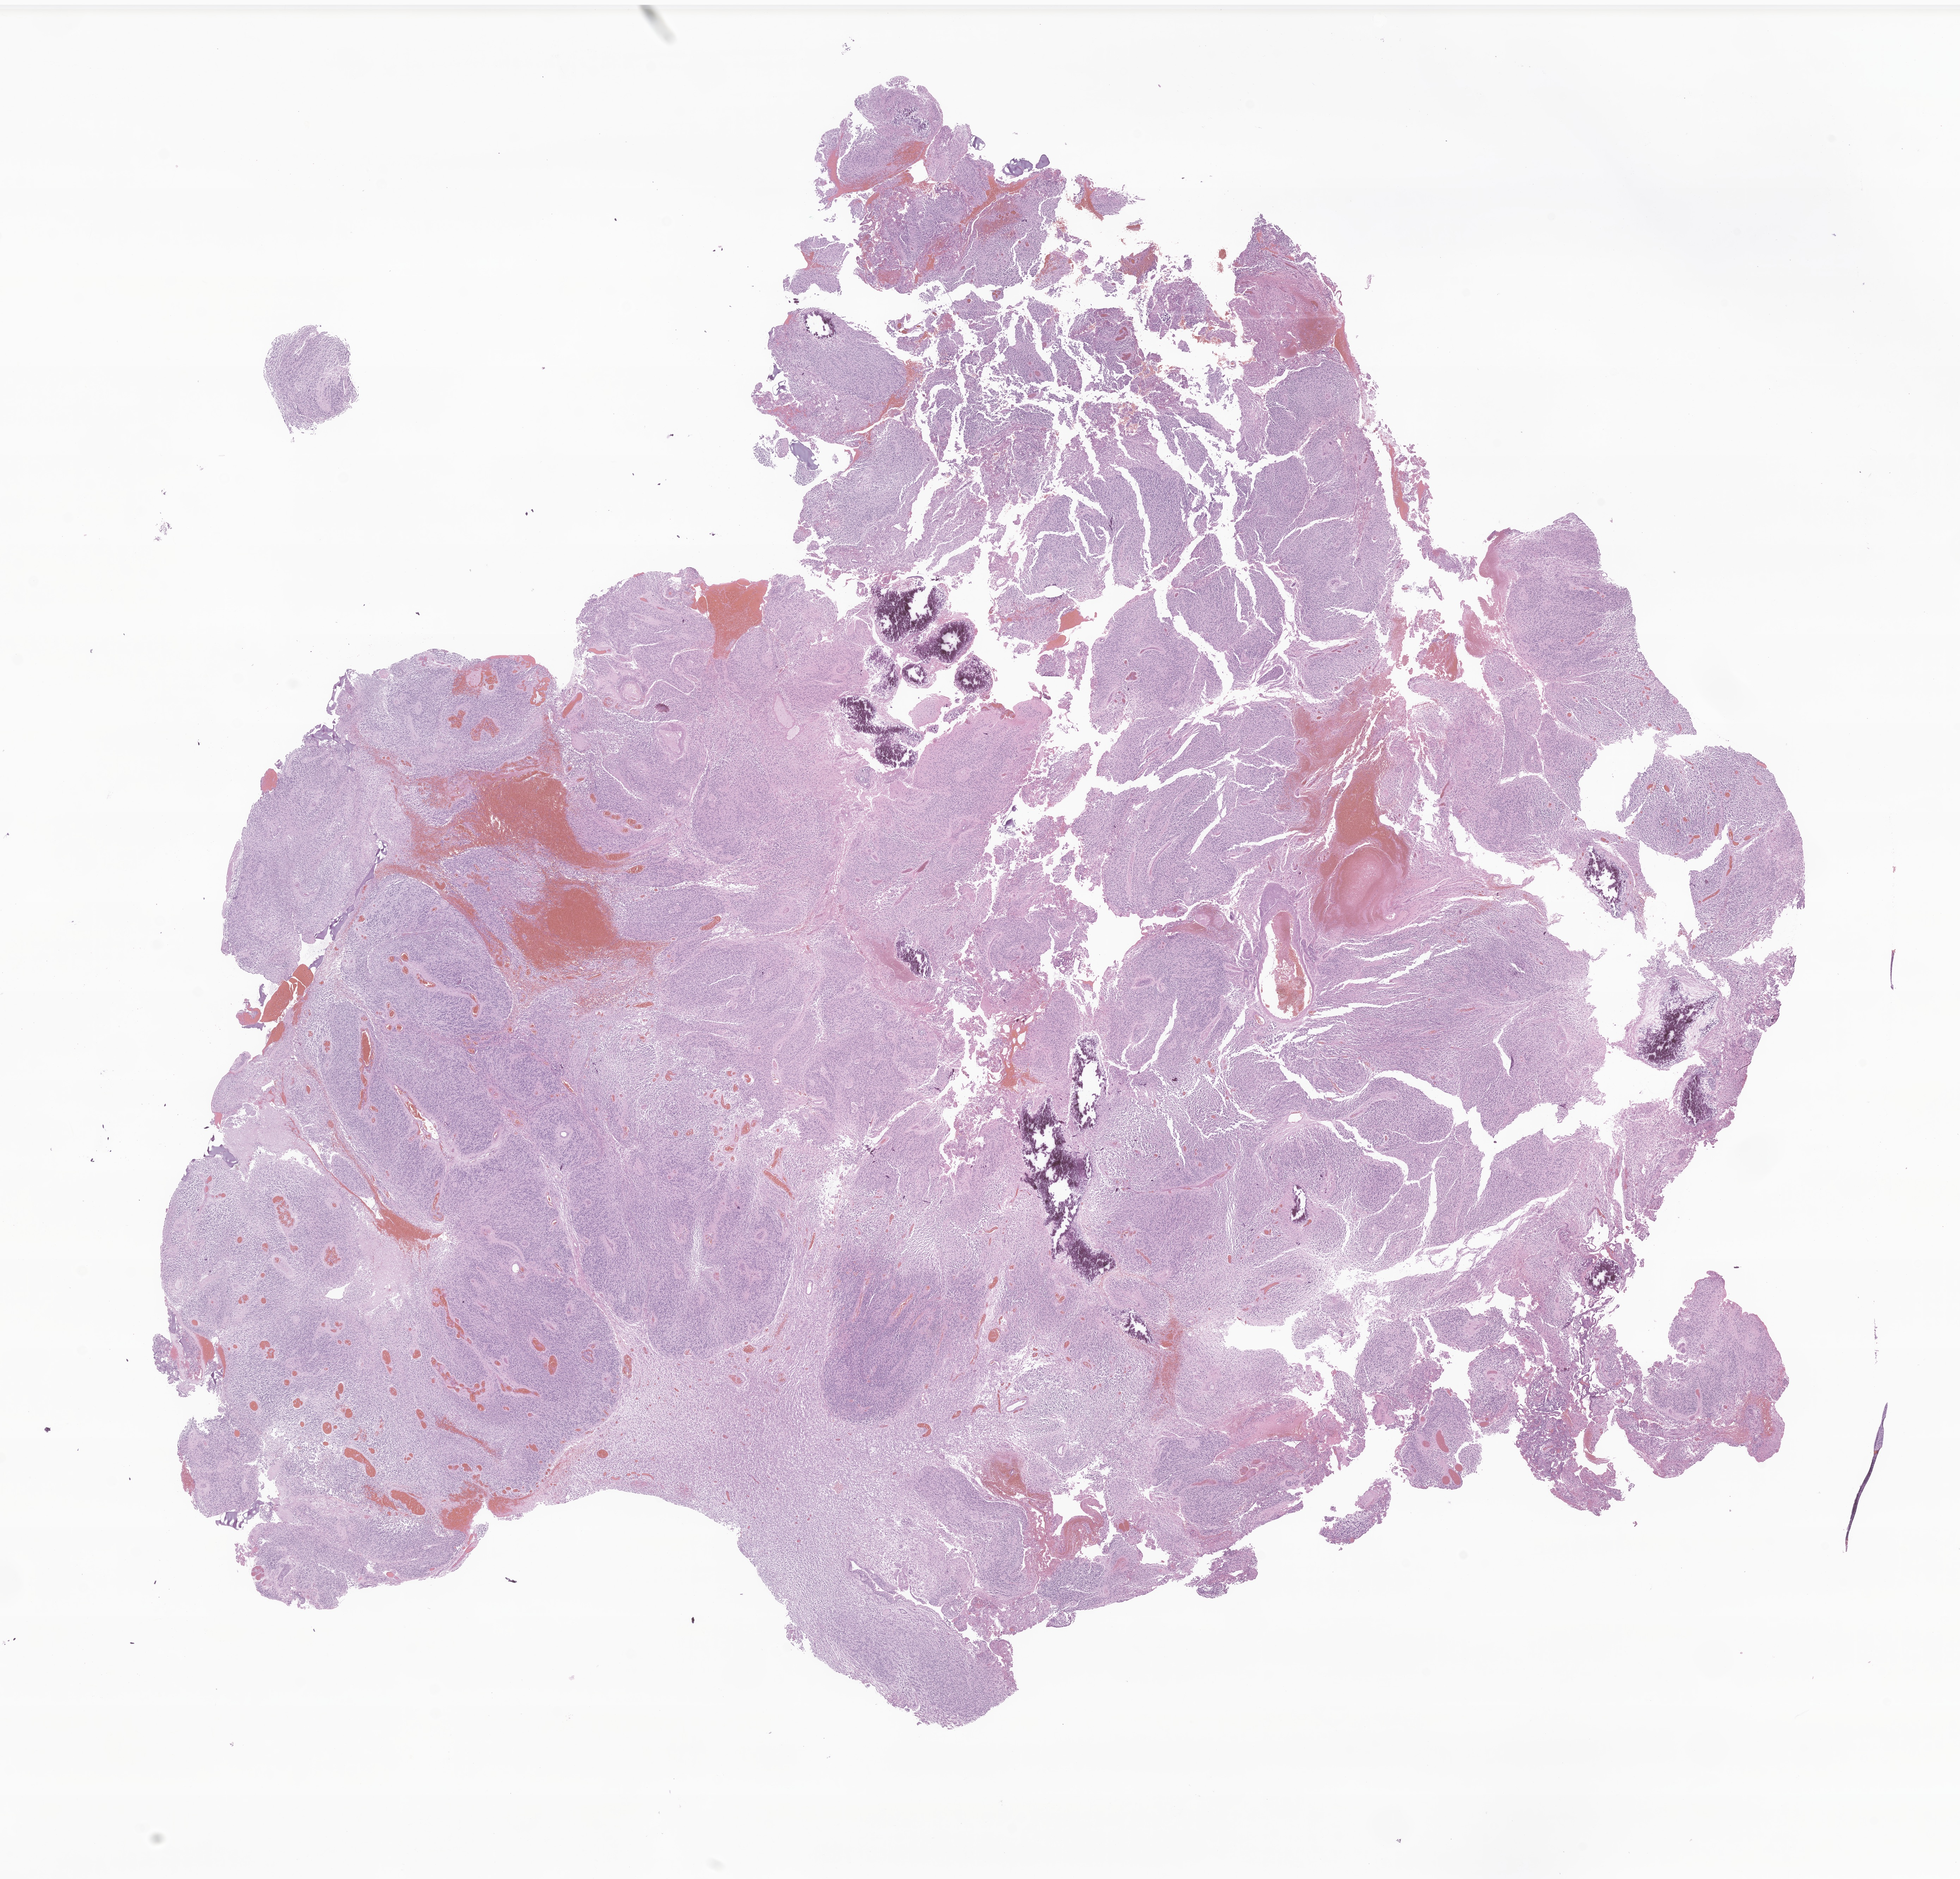
Digitized haematoxylin and eosin-stained section of tumor tissue from the brain — low-resolution overview of the scanned area, about 23.4 x 22.5 mm. Formalin-fixed paraffin-embedded section. Patient male; age 735 days (about 2.0 years).
• diagnosis: Glioblastoma, NOS